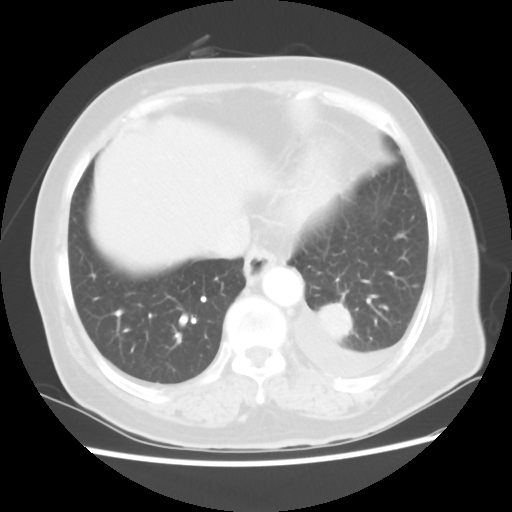
Chest CT, one axial slice; slice 11 of 80 in the series (ordered by position); reconstruction kernel STANDARD; 100 kVp; lung window (W 1500 / L -600 HU); 512 × 512 image matrix. Patient: female, 68 years. From the clinical record (not read from this slice): clinical TNM (as recorded): T1c N0 M1.
Annotated regions visible in this slice (rectangle marked by the reading radiologist):
- lung tumour (recorded histology: adenocarcinoma): bounding box [x1, y1, x2, y2] px = [318, 300, 362, 346]